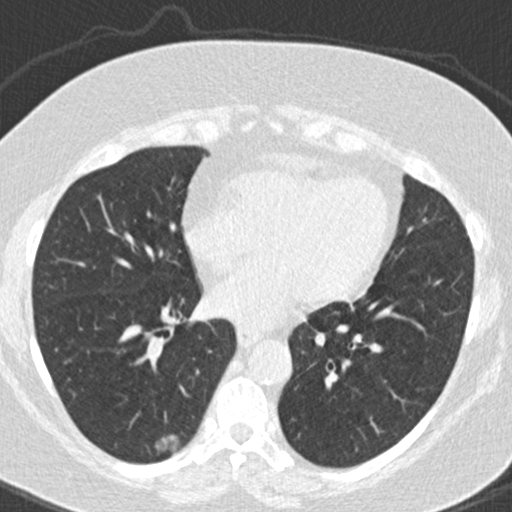
Low-dose screening chest CT, one axial slice; slice 73 of 177 in the series (ordered by position); 120 kVp; lung window (W 1500 / L -600 HU); 2 mm slice thickness; 512 × 512 image matrix.
Structures marked on this image (outlined manually by an expert reader):
- lesion 1 (tumor, lower lobe of right lung): bounding box [x1, y1, x2, y2] px = [155, 435, 181, 451]